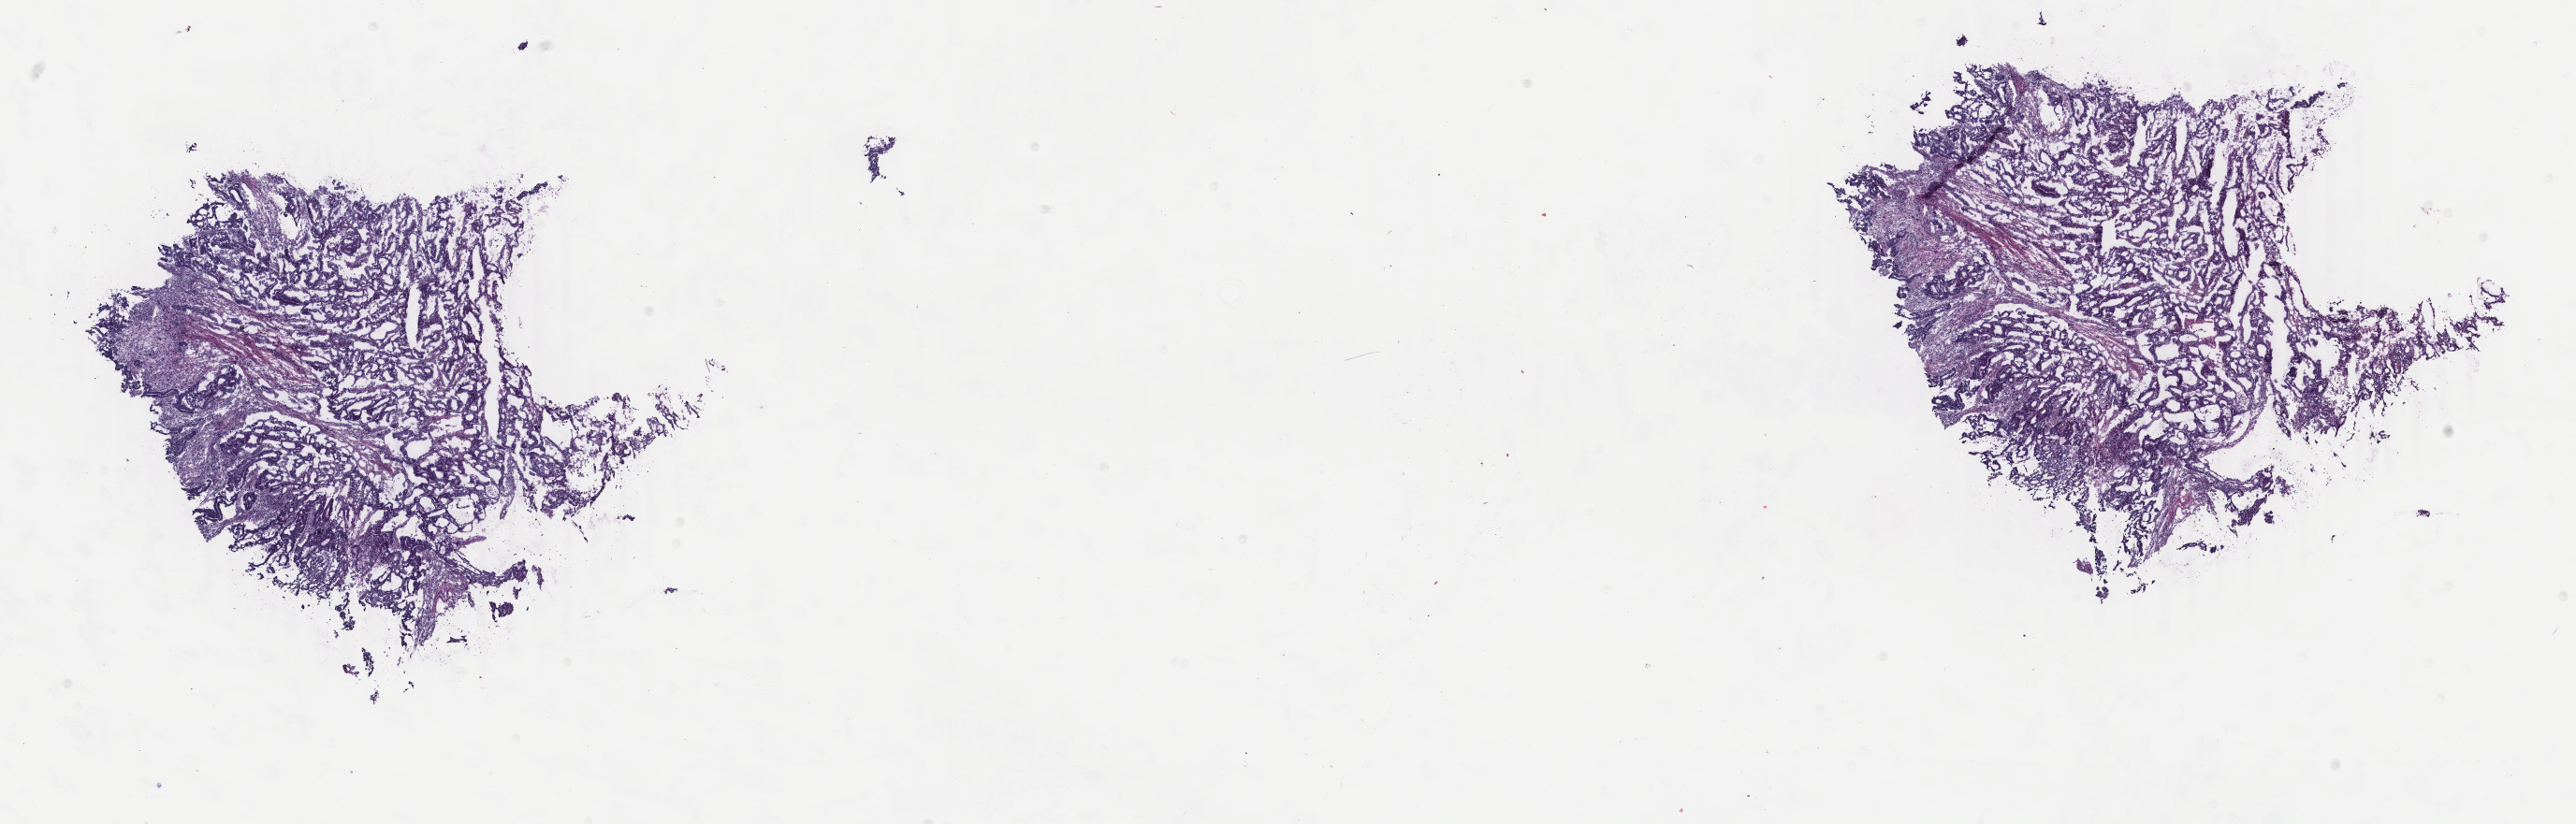
Digitized H&E-stained tissue section (whole slide), whole scanned area (about 21.9 x 7.0 mm, from a 40x scan) shown as a low-resolution overview, frozen section from the top of the tissue portion, sample: primary tumour, uterus. Female patient; age at initial diagnosis 63 years. Composition of this section per pathologist review: tumour cells 80%, tumour nuclei 65%.
Histologic diagnosis: Endometrioid adenocarcinoma, NOS (endometrium).